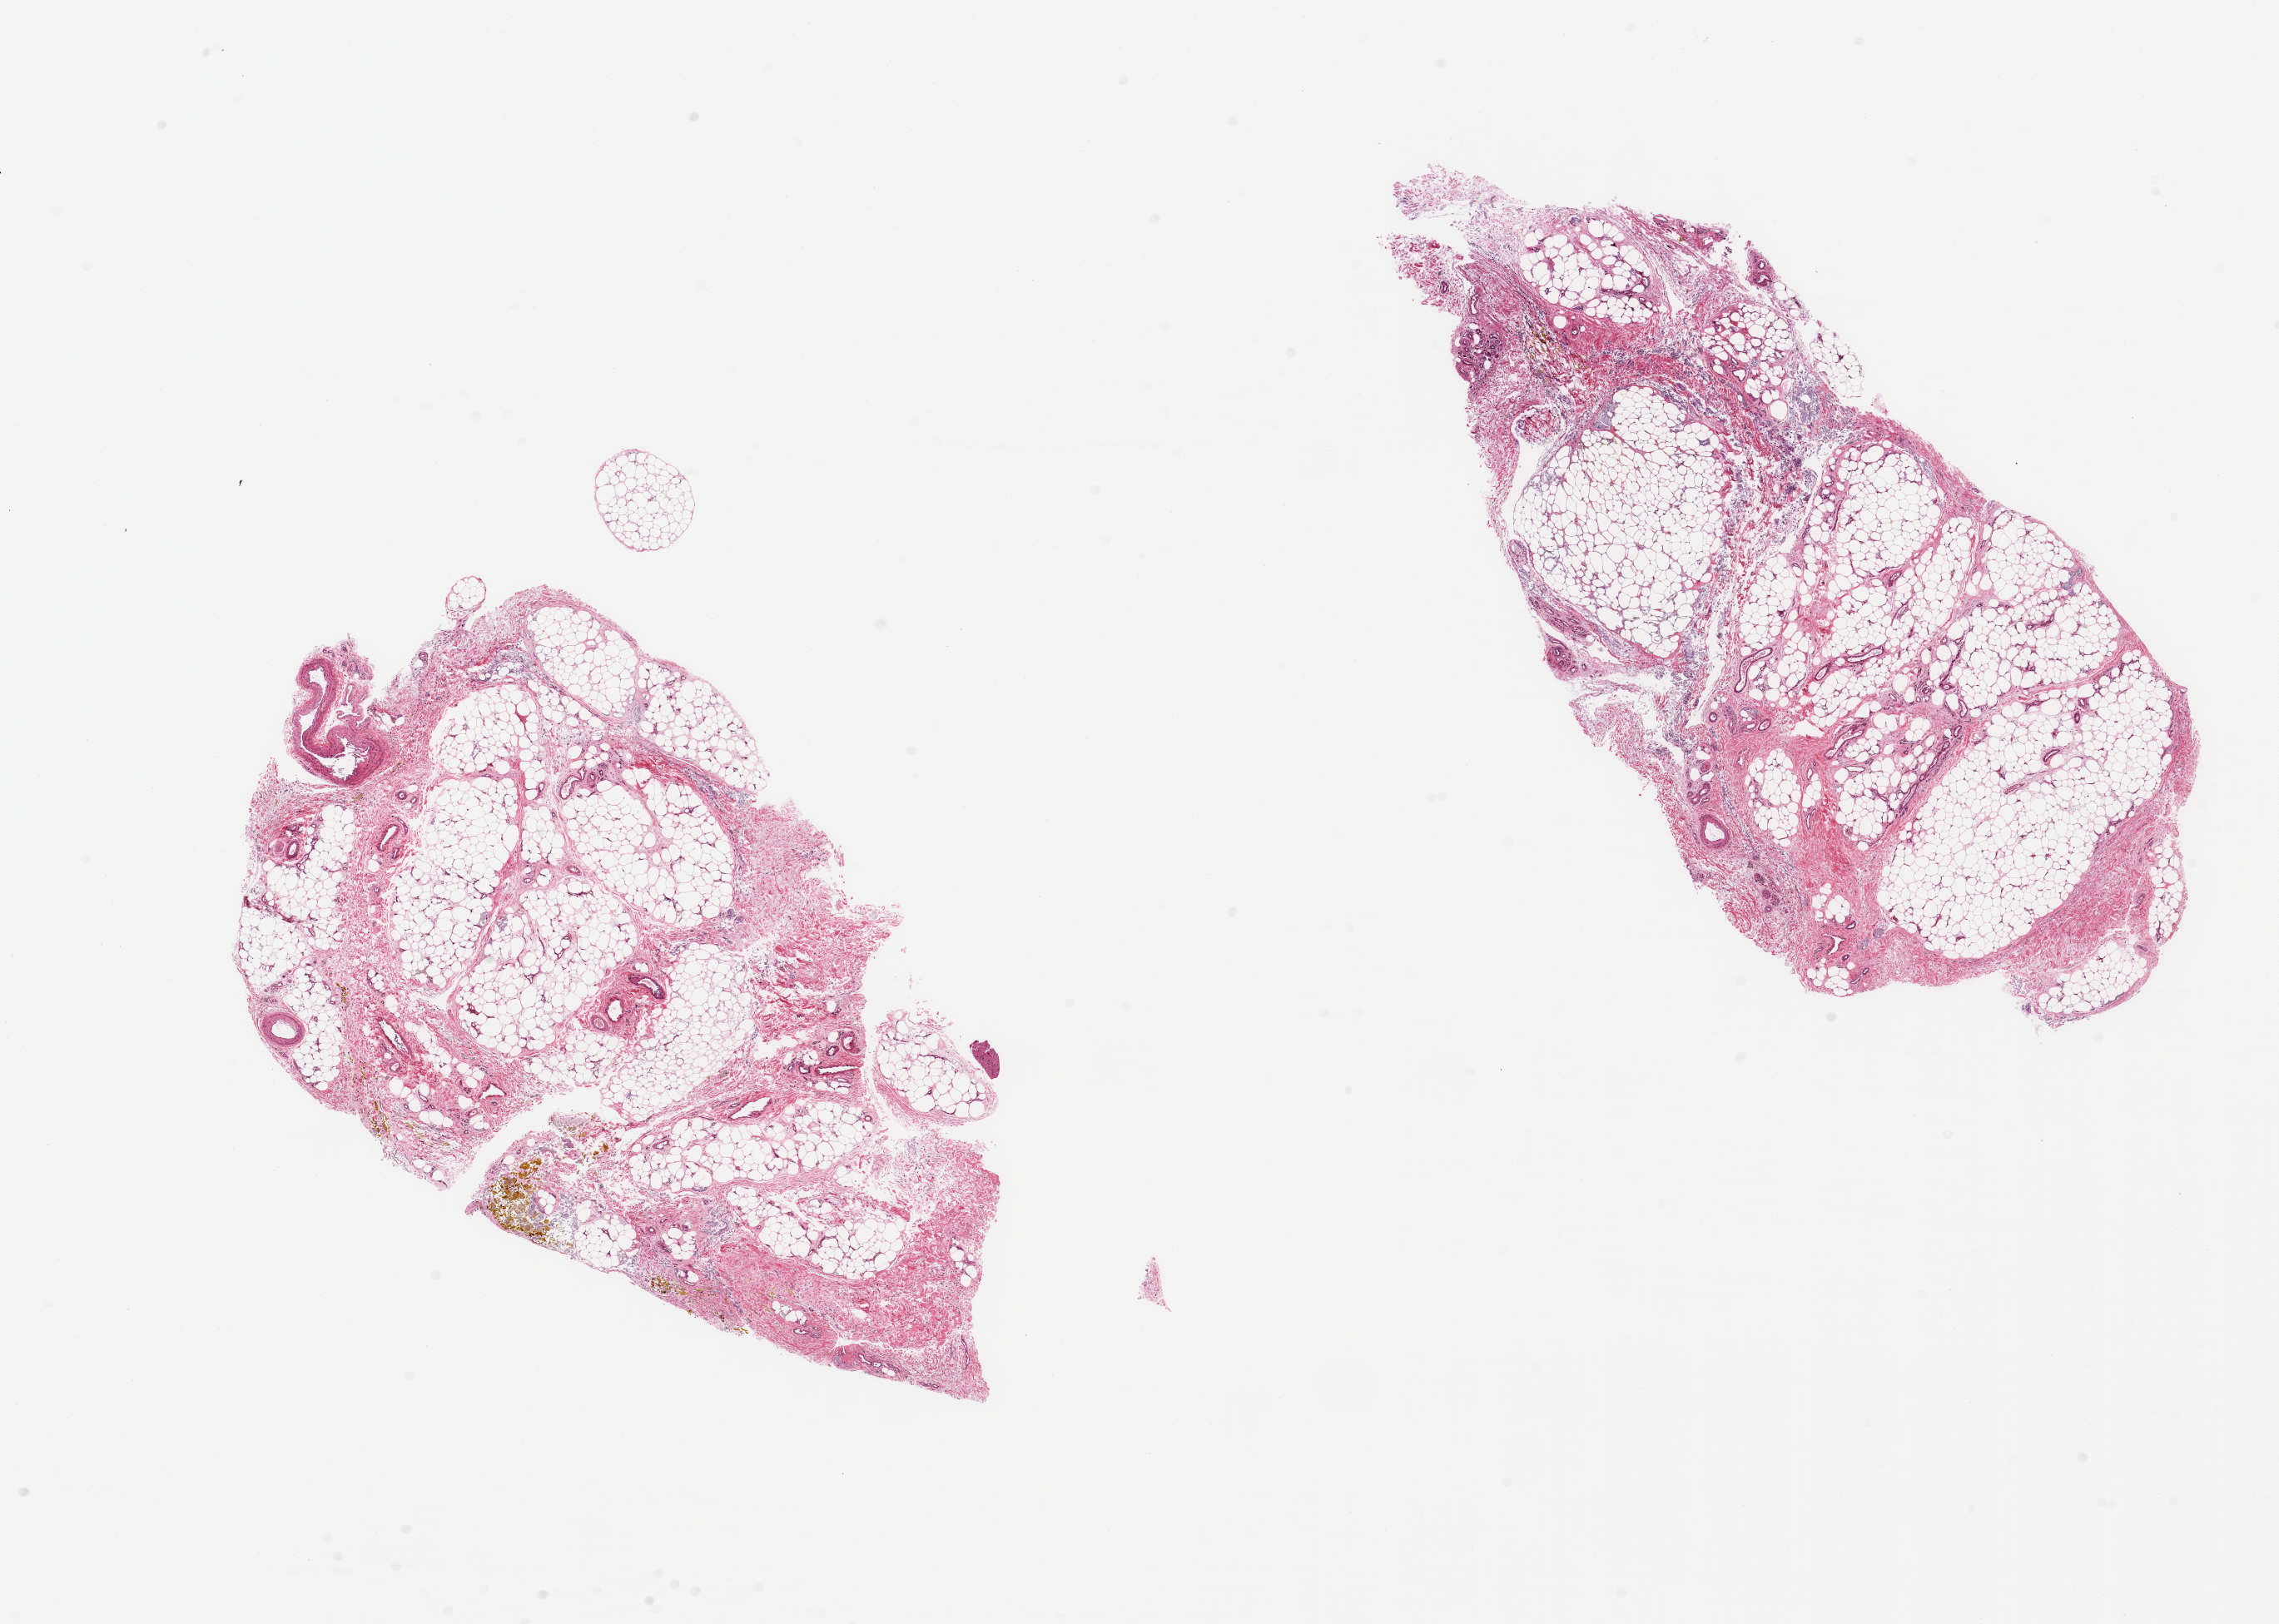
Digitized hematoxylin and eosin (H&E)-stained section, shown as a low-resolution overview of the whole scanned area (about 21.7 x 15.4 mm, slide scanned at 20x); PAXgene-fixed, paraffin-embedded tissue; target tissue: adipose tissue; donor tissue sample. Donor sex: male.
Reviewer comment on this tissue sample: 2 pieces, ~60% fascia/vascular elements; foreign pigmented material, unknown provenance (?tattoo?).